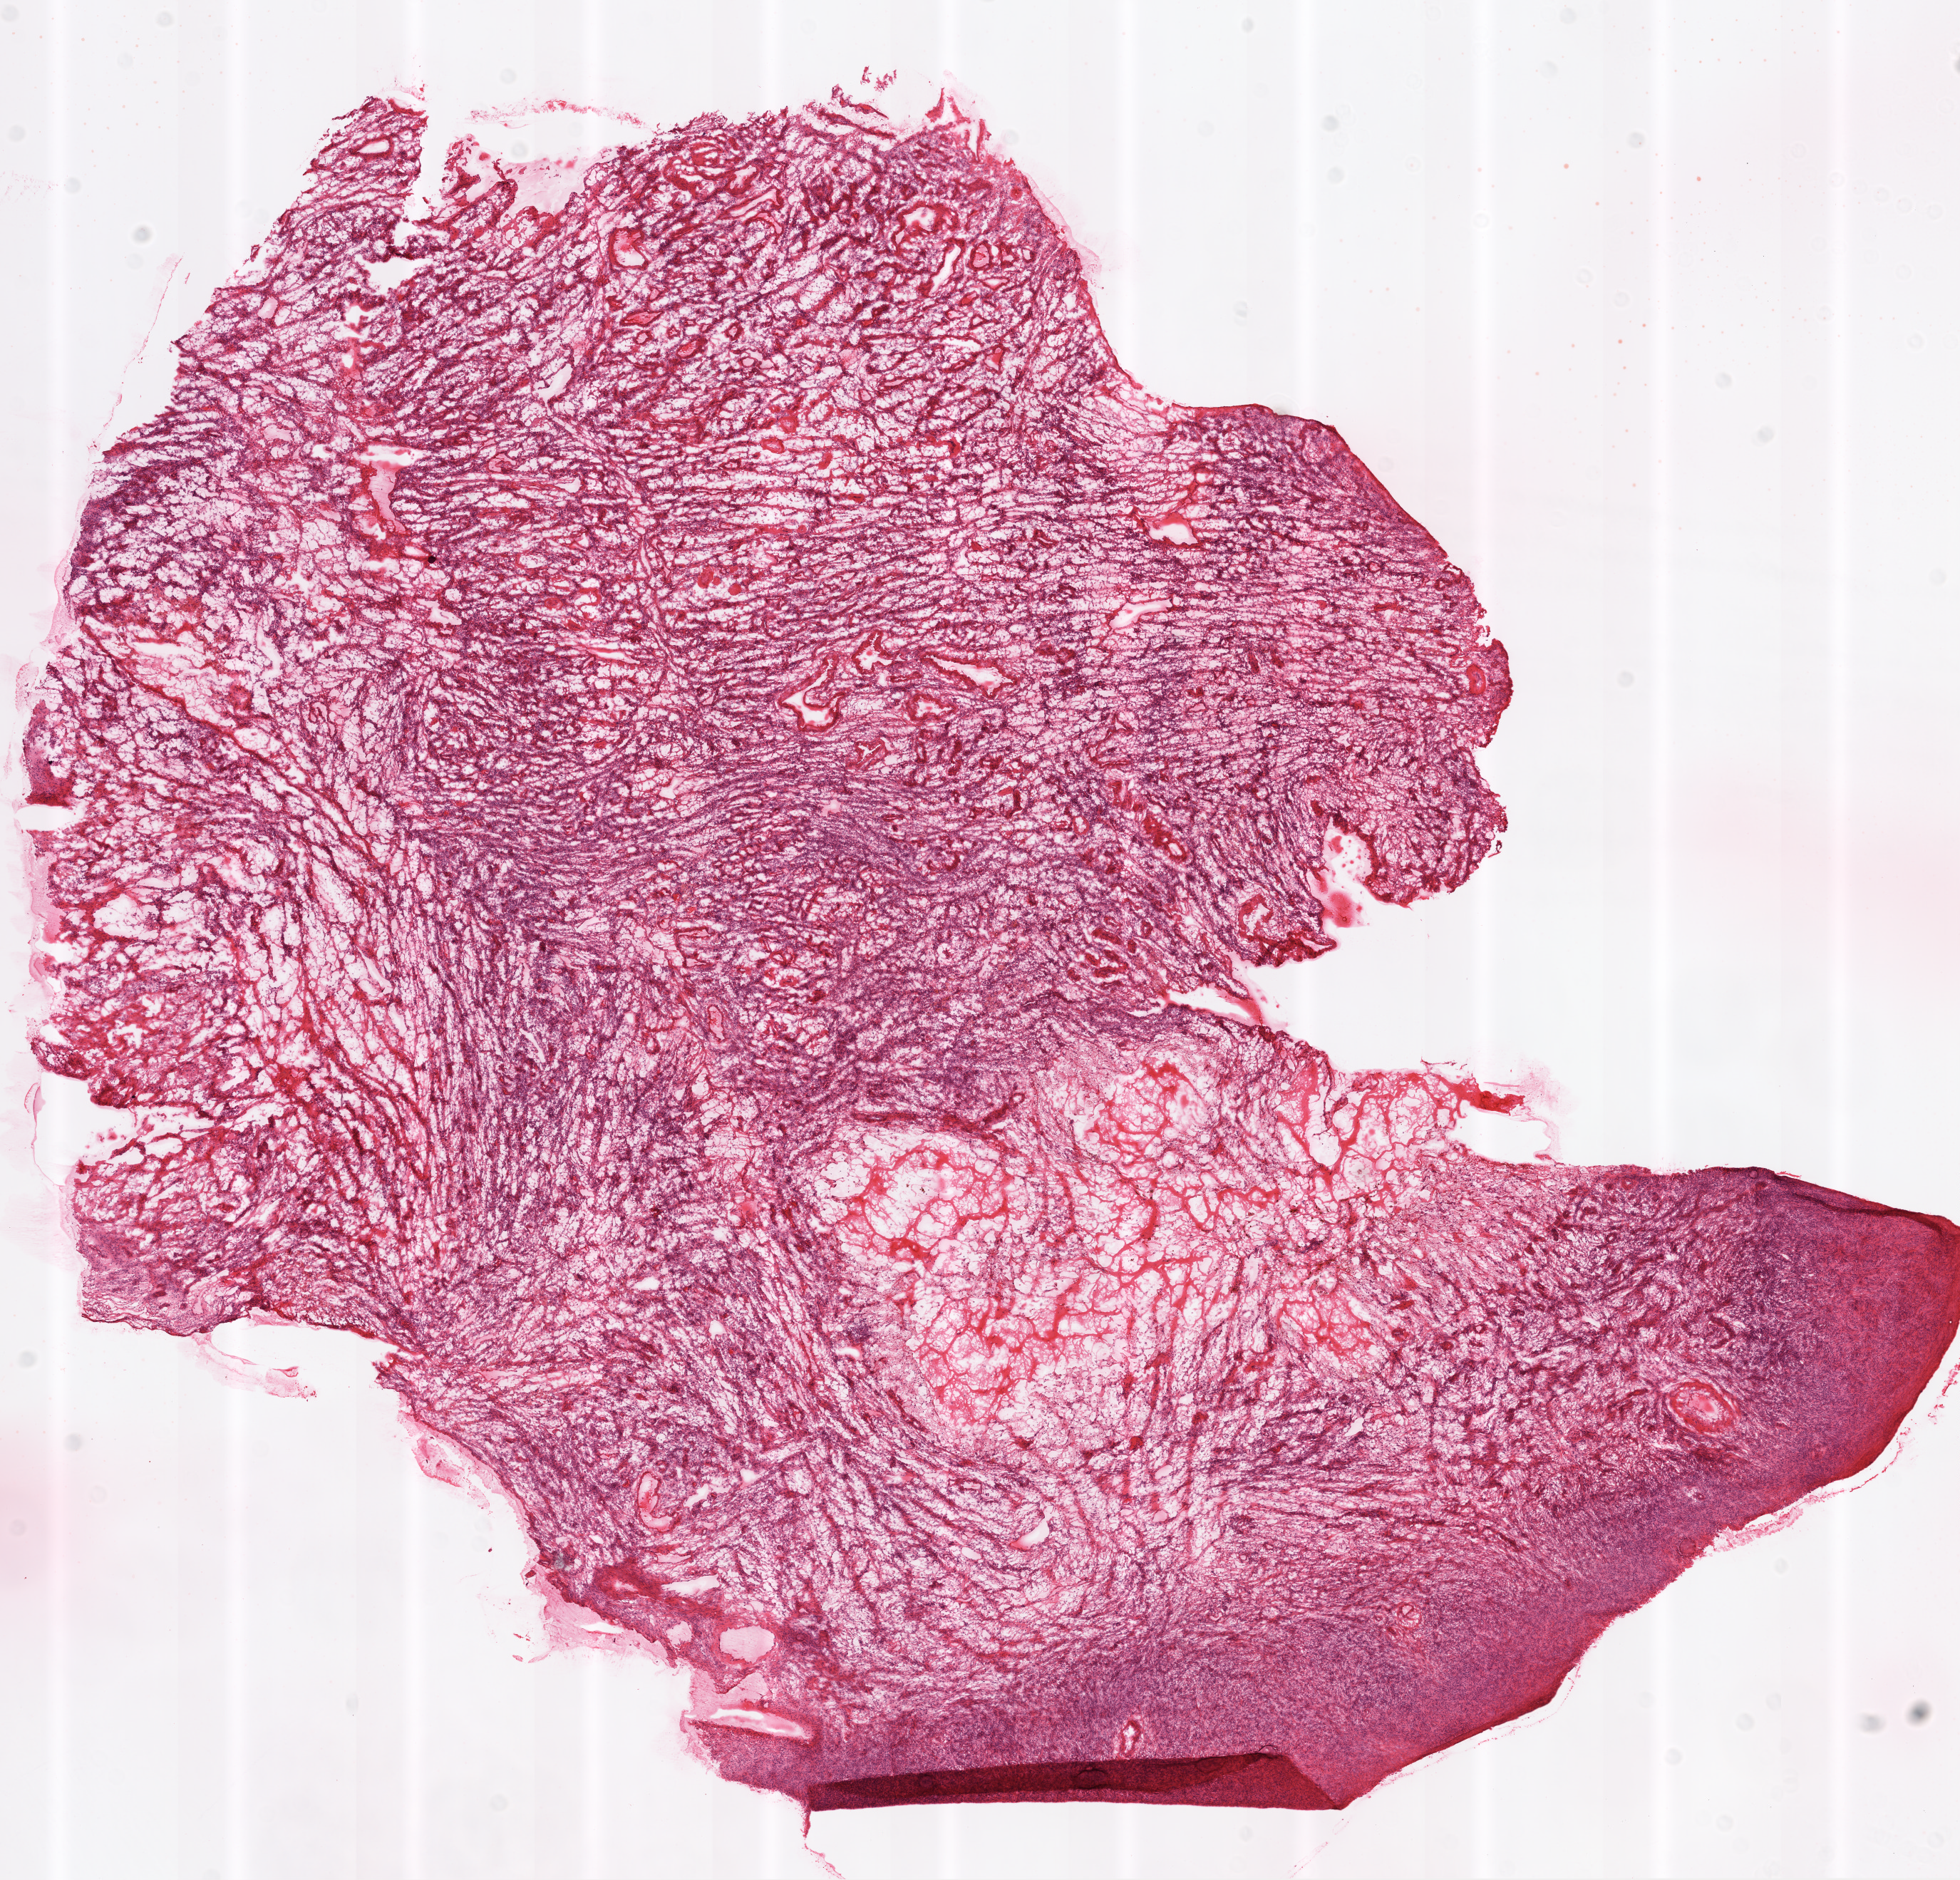
Whole-slide histology image, Hematoxylin and eosin (H&E) stained, low-resolution overview of the scanned area, about 11.0 x 10.6 mm (slide scanned at 20x), frozen section from the top of the tissue portion, primary tumour sample from the ovary. Patient: female, age at initial diagnosis 38 years. Histologic grade: G1 (well differentiated). Slide review estimates, as recorded: tumour cells 85%, tumour nuclei 80%, normal cells 0%, stromal cells 0%, necrosis 15%.
• laterality: bilateral
• FIGO stage: IV
• pathologic diagnosis: Serous cystadenocarcinoma, NOS